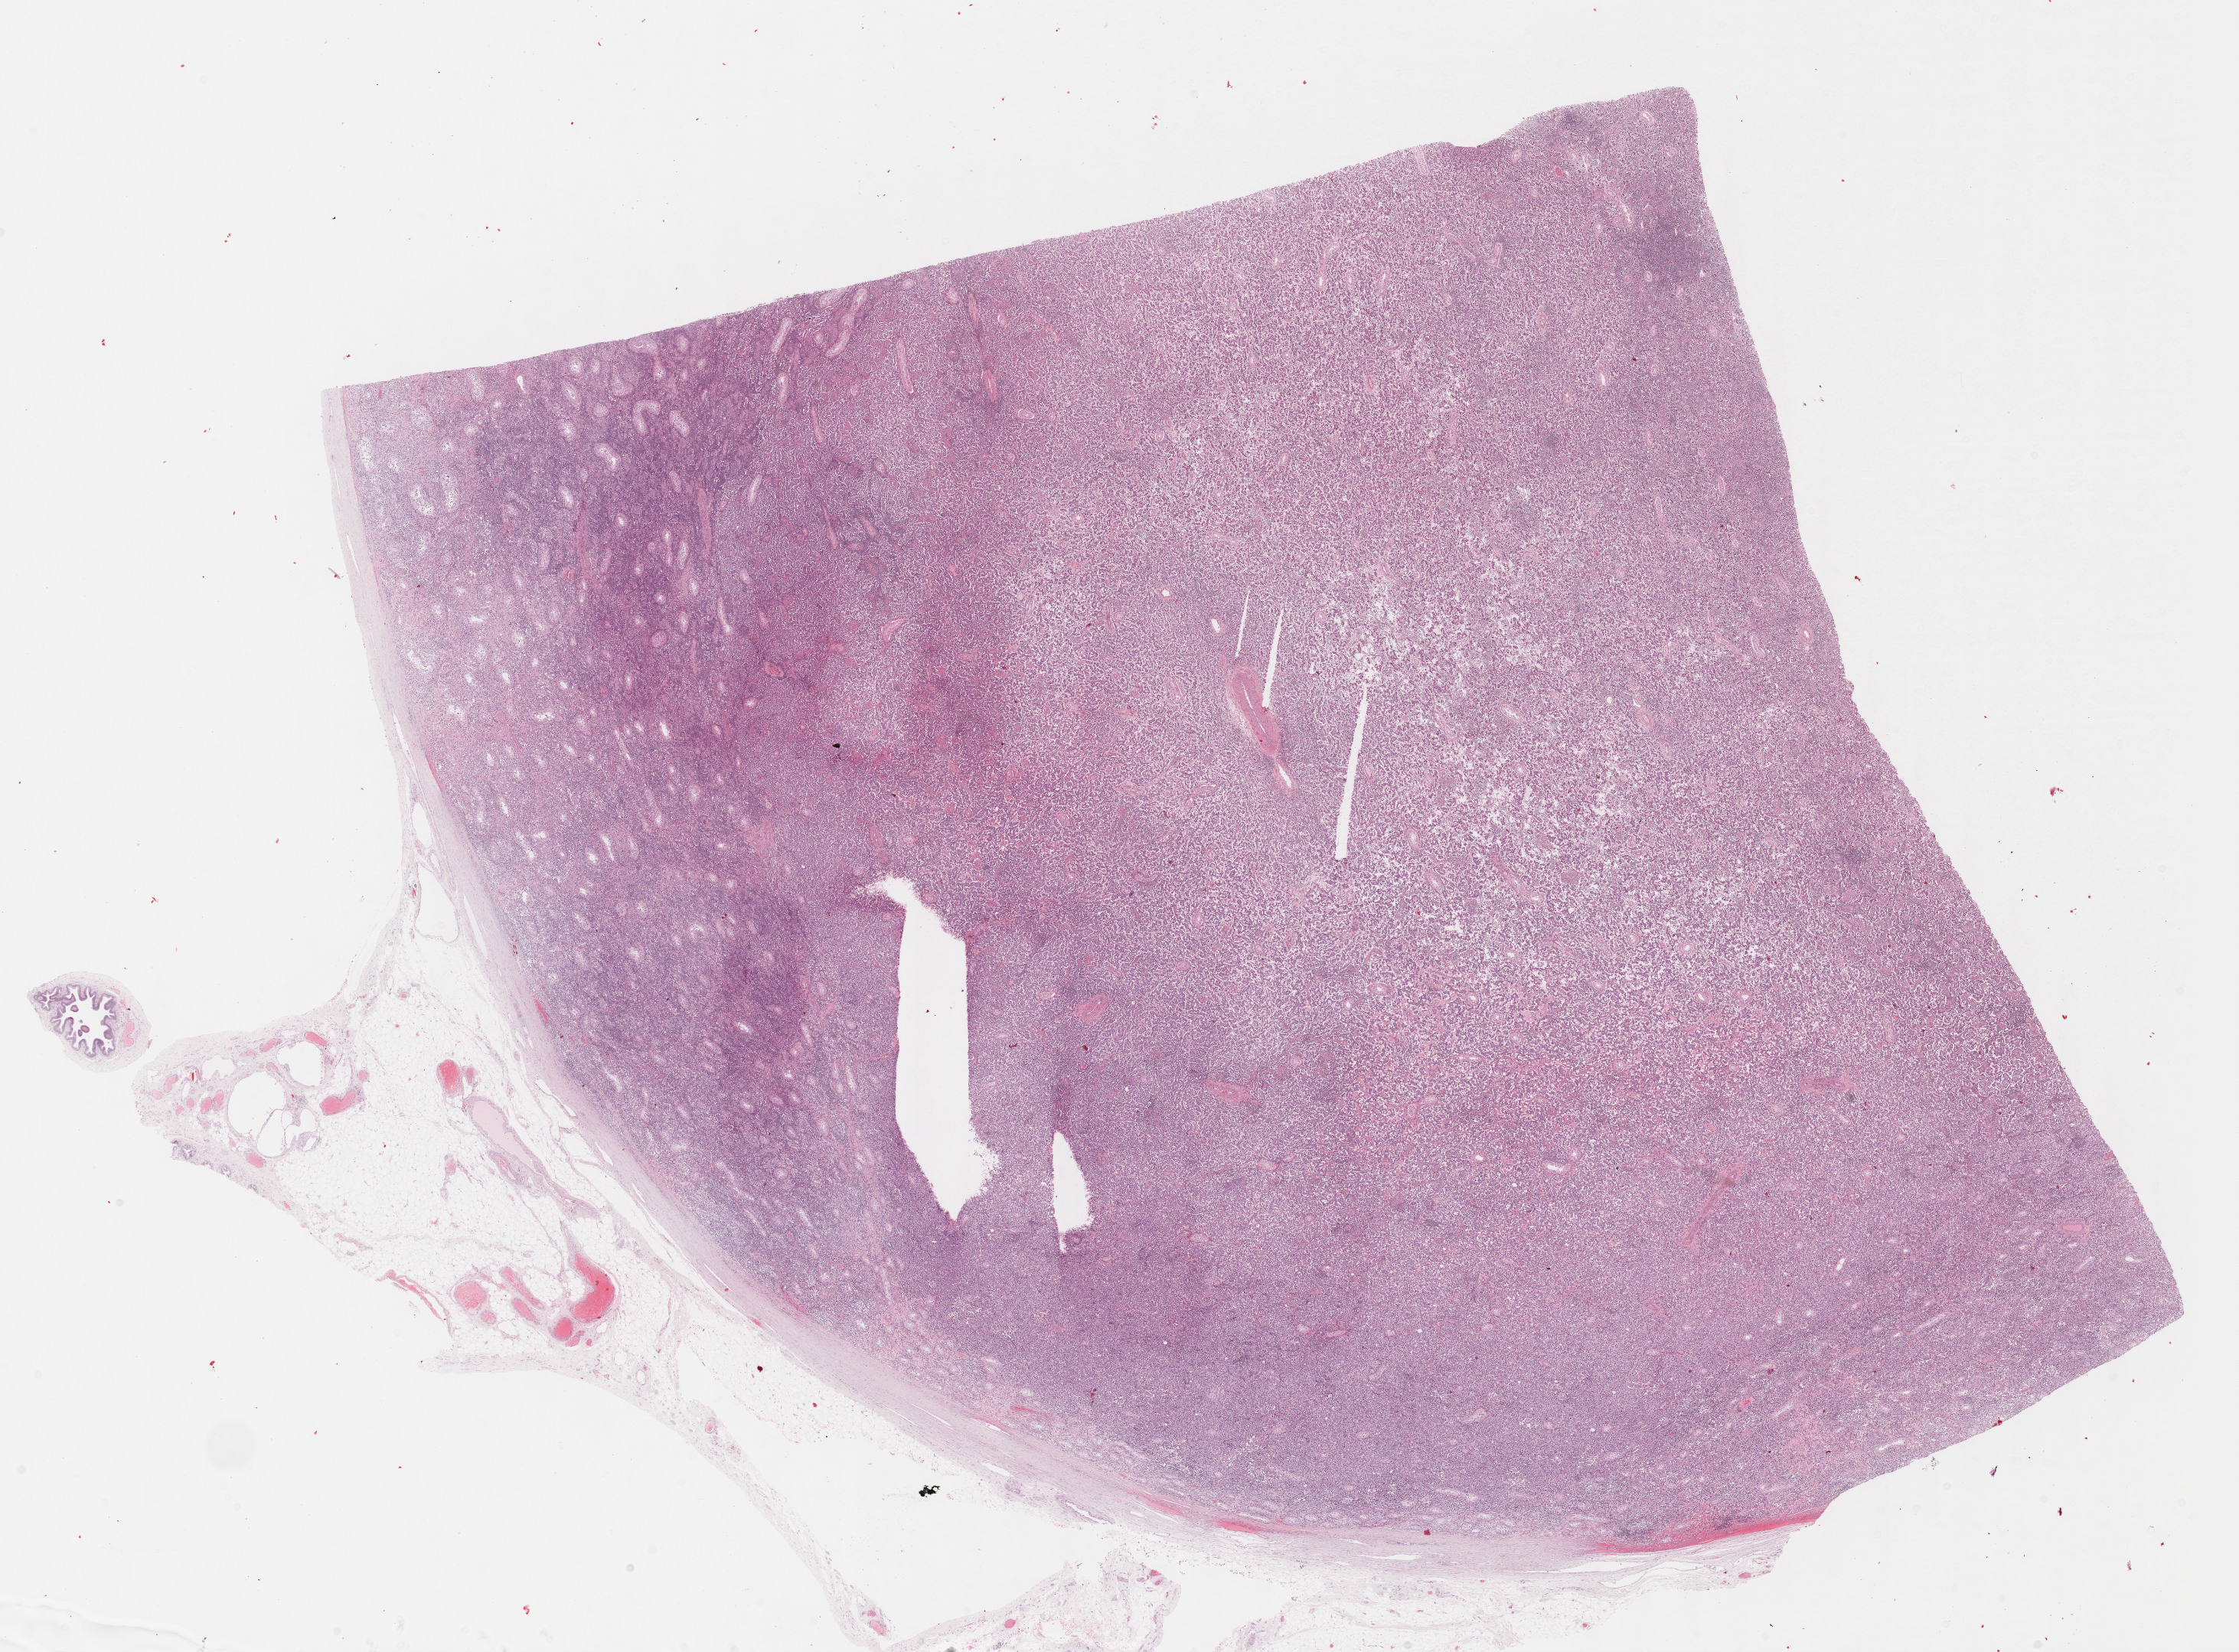
Whole-slide histology image, Hematoxylin and eosin (H&E) stained, a low-resolution overview of the entire scanned area, about 23.6 x 17.4 mm (acquisition: 40x scan); formalin-fixed paraffin-embedded (FFPE) diagnostic section; sample: primary tumour, testis. Male, age 34 years at initial diagnosis.
- histologic diagnosis: Seminoma, NOS
- AJCC pathologic stage: IA (7th edition)